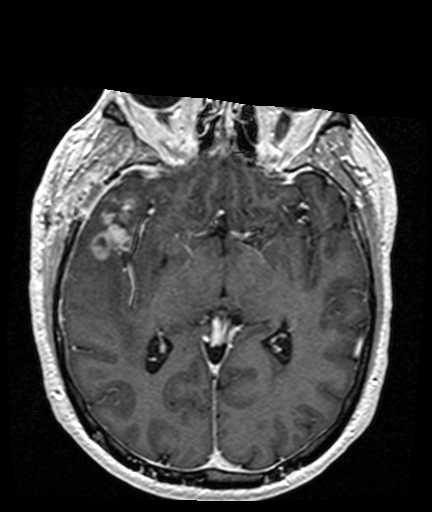
Brain MRI from a brain-tumour surgery series, one axial slice; T1-weighted post-contrast; 1 mm slice thickness; 432 × 512 image matrix, field of view 194 × 230 mm. From the clinical record (not read from this slice): histopathology: Glioblastoma; WHO grade: 4; IDH mutation: no.
Structures marked on this image (expert manual segmentation):
- tumour: bounding box [x1, y1, x2, y2] px = [92, 196, 144, 261]